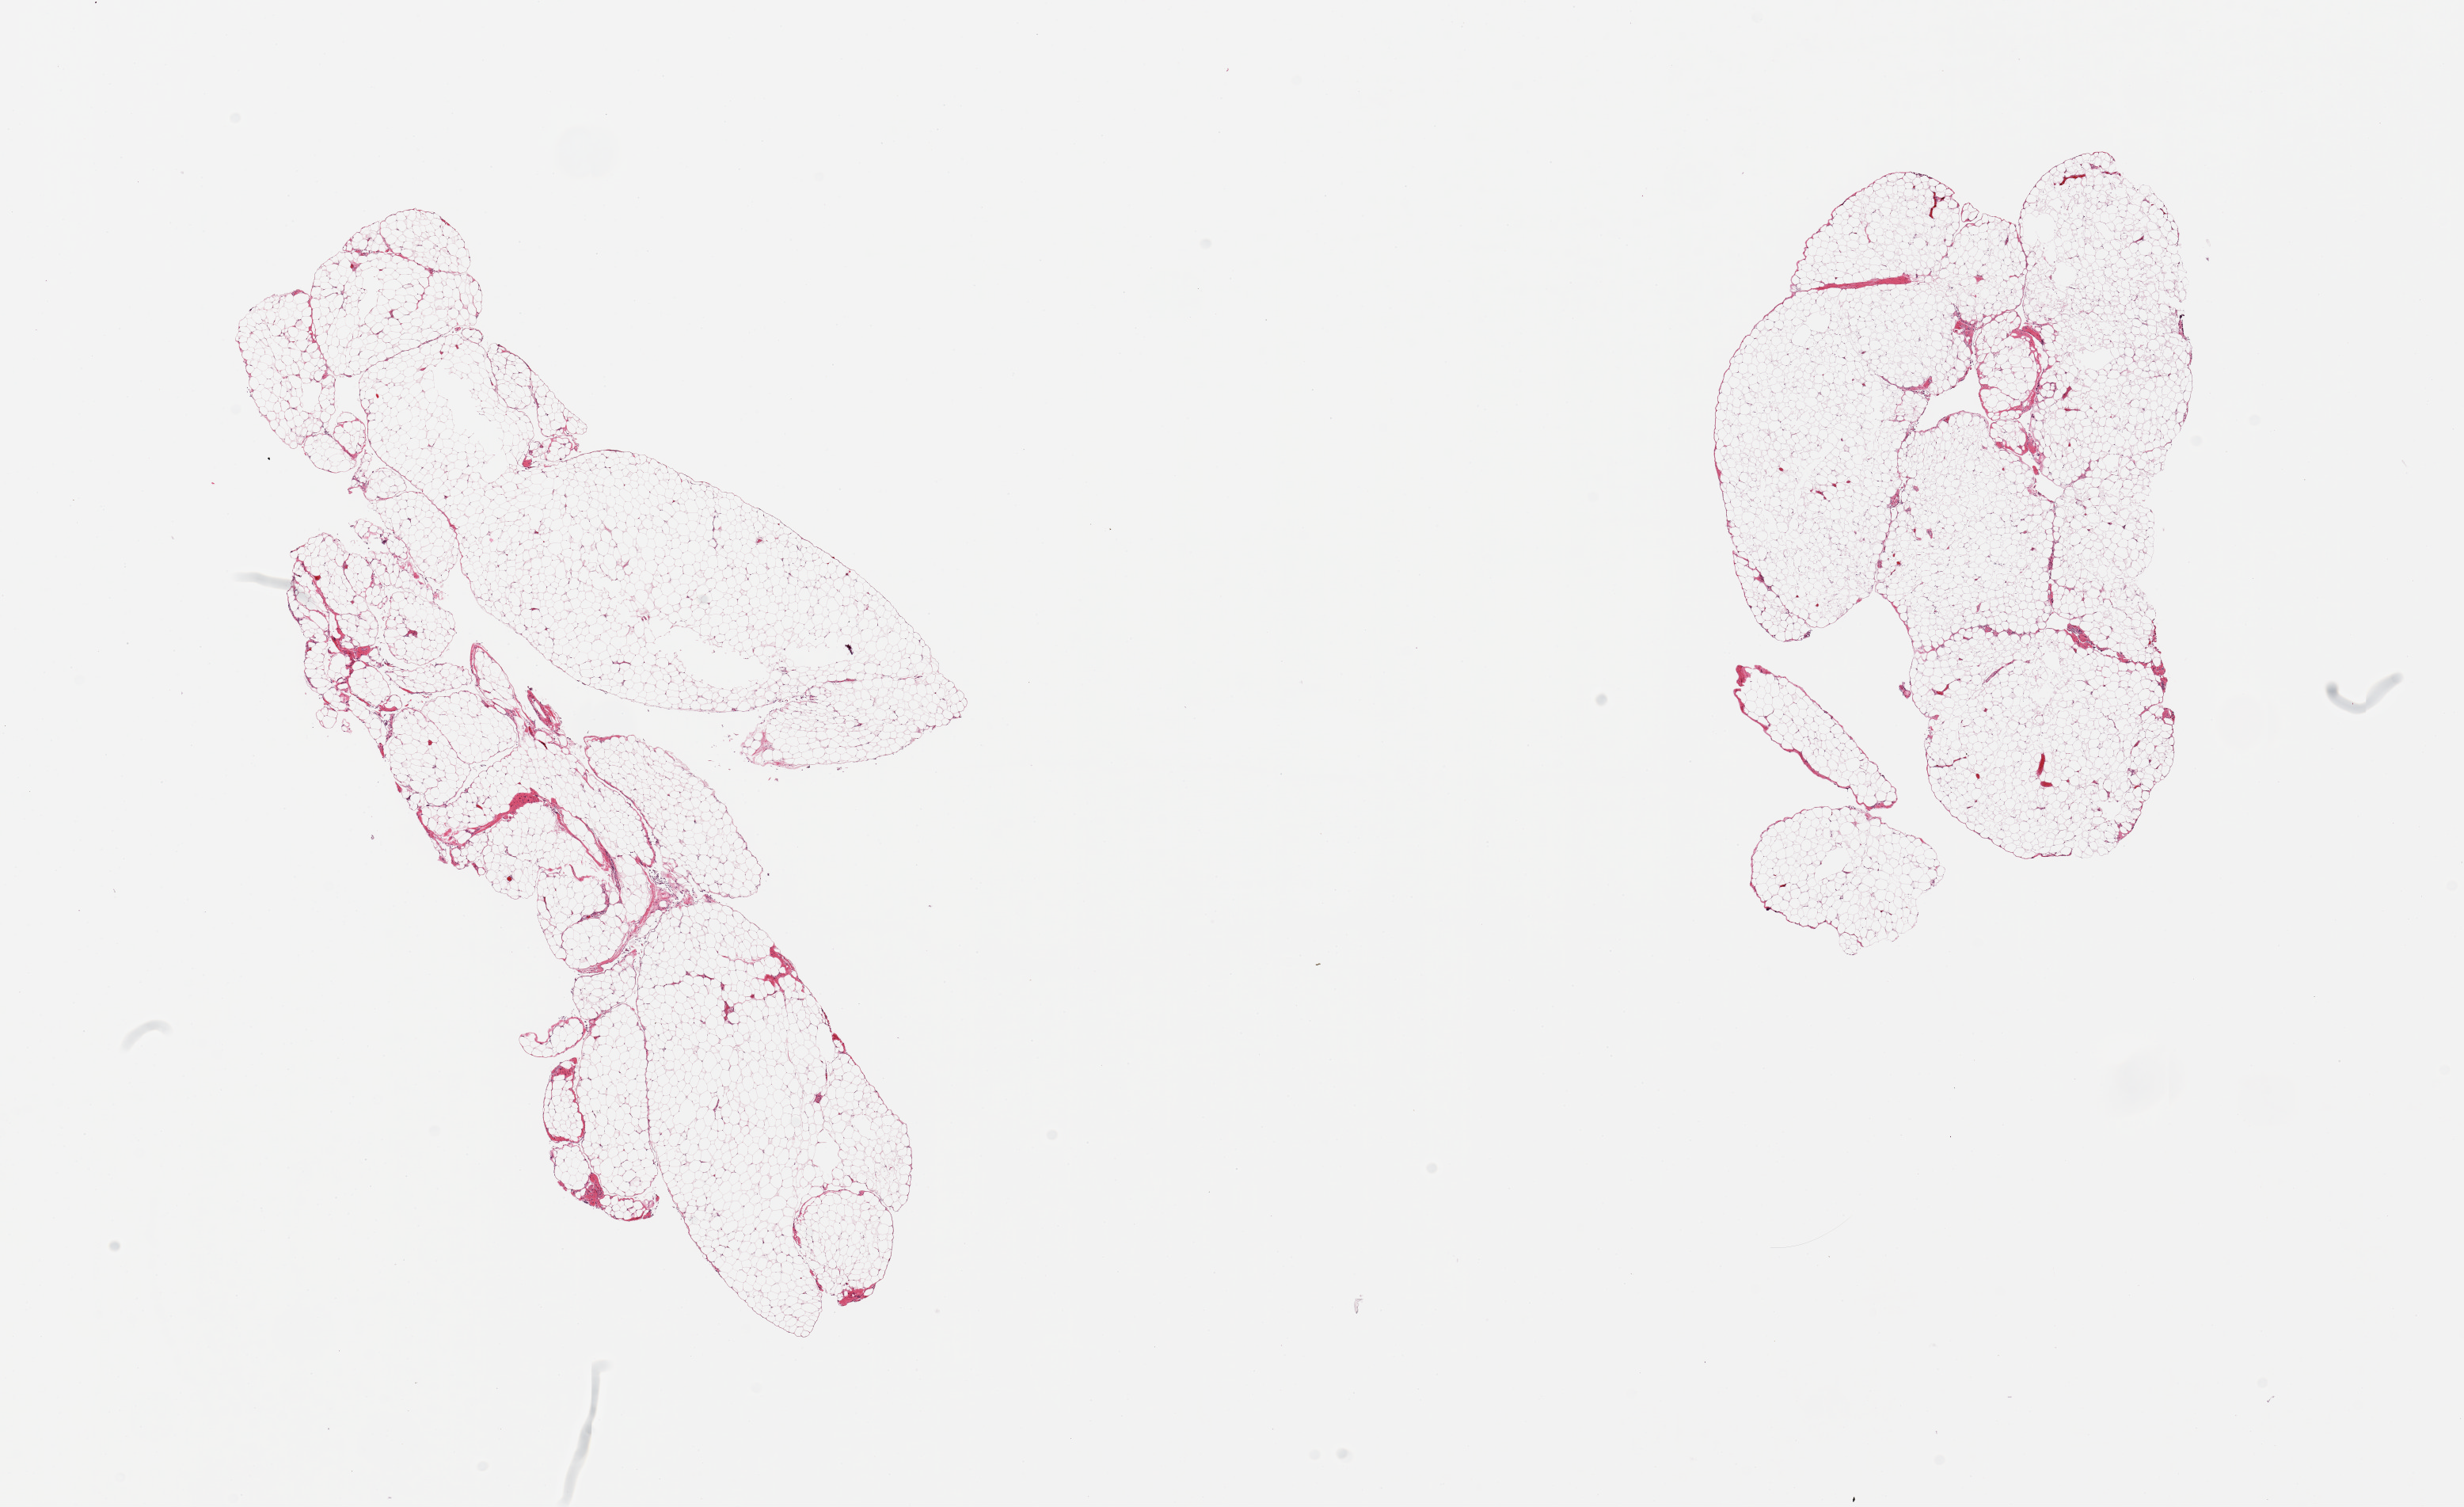
Digitized haematoxylin and eosin-stained section, whole scanned area (about 24.6 x 15.0 mm, slide scanned at 20x) shown as a low-resolution overview. PAXgene-fixed, paraffin-embedded tissue. Section of omentum (target tissue). Donor tissue sample. Donor: male.
Pathologist's review note for this sample: 2 pieces.